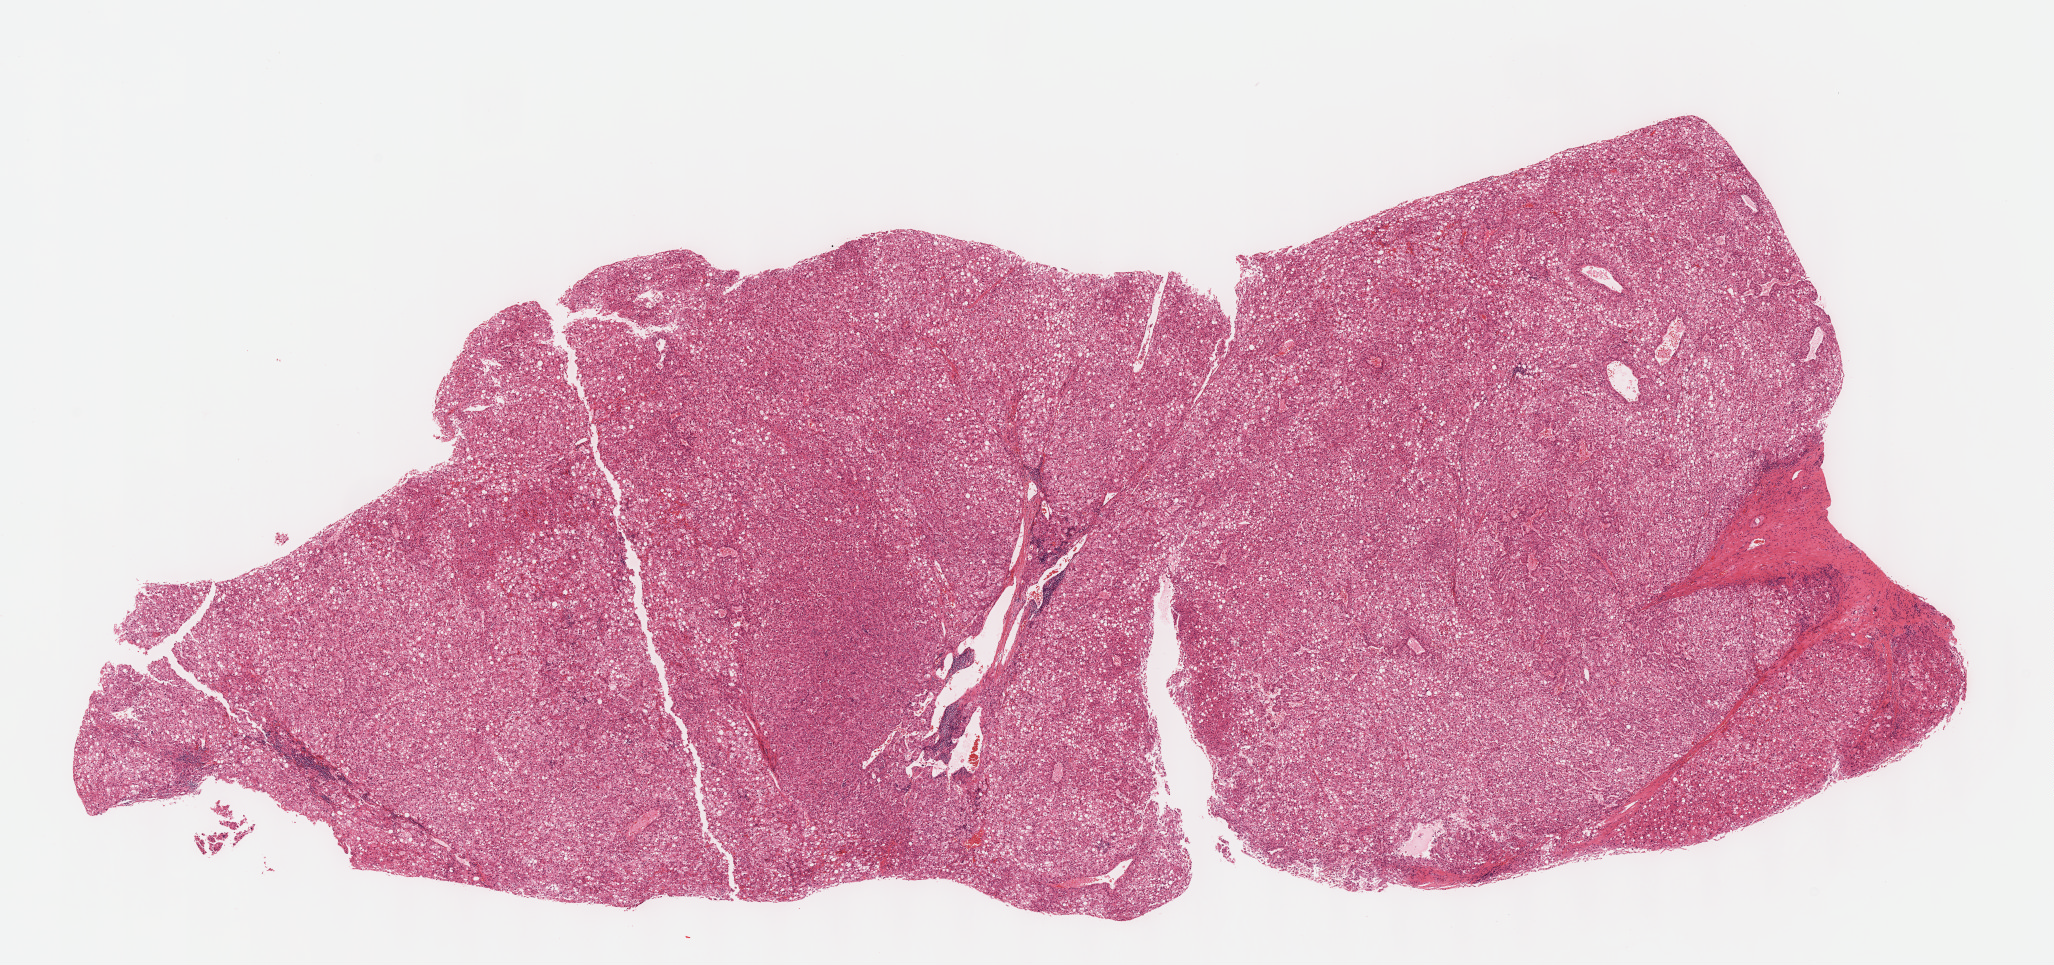
Digitized Hematoxylin and eosin (H&E) stained tissue section (whole slide), low-resolution overview of the scanned area, about 16.6 x 7.8 mm (slide scanned at 40x); formalin-fixed paraffin-embedded (FFPE) diagnostic section; primary tumour sample from the liver. Female patient; age at initial diagnosis 69 years. Histologic grade: G2 (moderately differentiated).
• pathologic diagnosis: Hepatocellular carcinoma, NOS
• TNM: T1 N0 M0
• AJCC pathologic stage: I (7th edition)